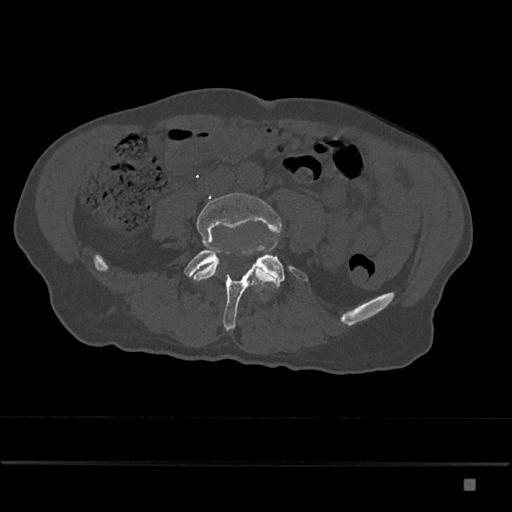
CT including the spine, one axial slice; slice 305 of 797 in the series (ordered by position); reconstruction kernel Br40s/3; bone window (W 1800 / L 400 HU); 512 × 512 image matrix, field of view 390 × 390 mm. Male patient, age 72 years. Case-level facts recorded for this patient, not image findings: primary cancer: prostate.
Outlined on this slice (semi-automatic segmentation, software-assisted and operator-edited):
- L4 vertebra: bounding box (x1, y1, x2, y2) in pixels: (191, 193, 282, 285)
- L5 vertebra: (184, 234, 308, 330)